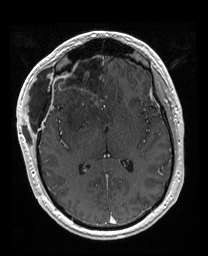
Brain MRI from a brain-tumour surgery series, one axial slice. T1-weighted post-contrast. 208 × 256 image matrix. Case-level facts recorded for this patient, not image findings: histopathology: Astrocytoma; WHO grade: 4; IDH mutation: yes.
Outlined on this slice (expert manual segmentation):
- previous resection cavity: bounding box (x1, y1, x2, y2) in pixels: (56, 52, 106, 111)